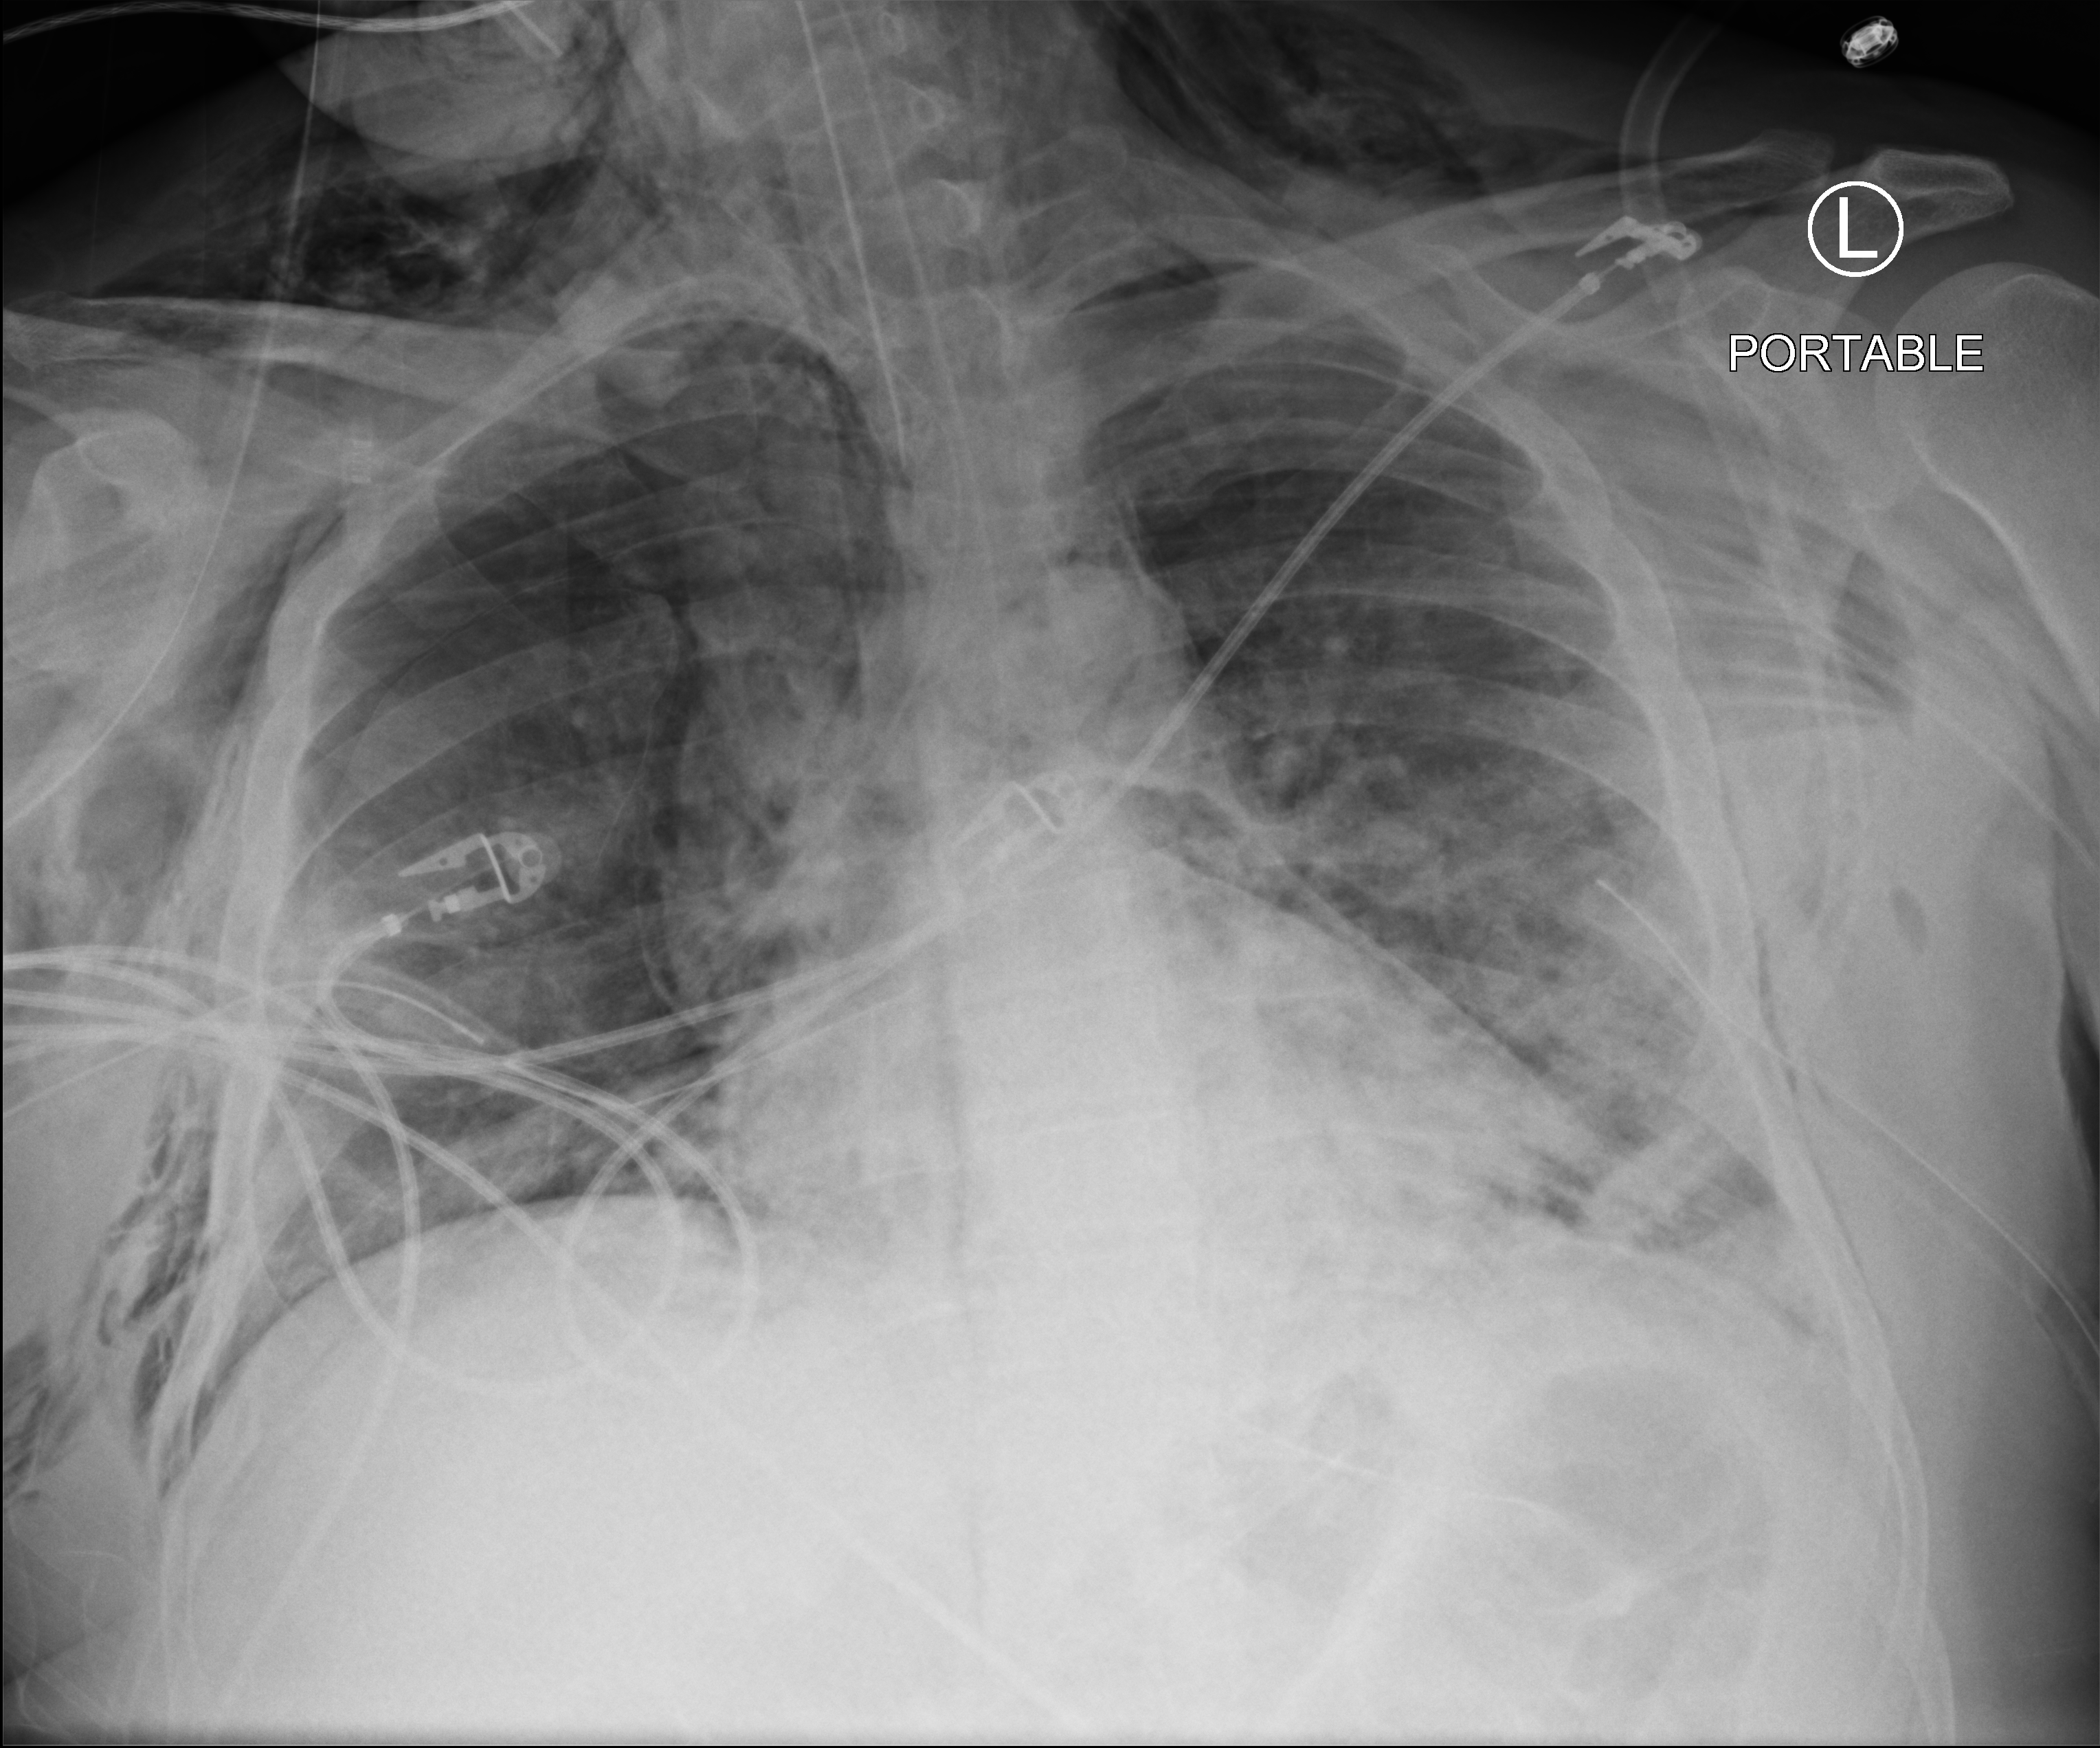
Portable chest radiograph. Male patient hospitalised with COVID-19, age 18–59 years.
Admission-level facts for this patient (not findings on this image; timing relative to this image not recorded): COPD (admission record): no.